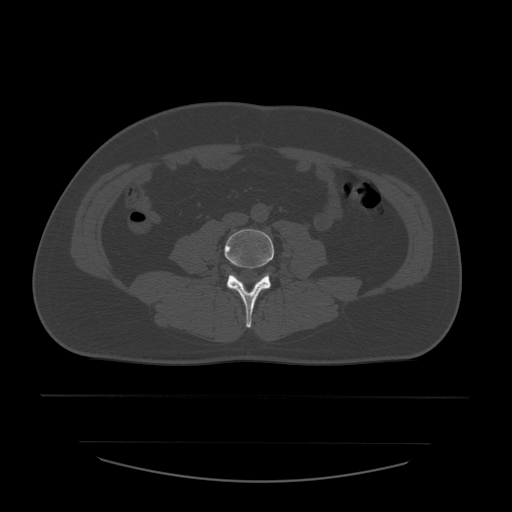
CT including the spine, one axial slice; position 143 of 532 along the scan axis; reconstruction kernel STANDARD; 120 kVp; bone window (W 1800 / L 400 HU); 512 × 512 image matrix. Patient age 44 years. Case-level facts recorded for this patient, not image findings: primary cancer: soft tissue sarcoma.
Structures marked on this image (semi-automatically segmented with operator editing):
- L4 vertebra: bounding box <225,229,274,328> (left, top, right, bottom; pixels)